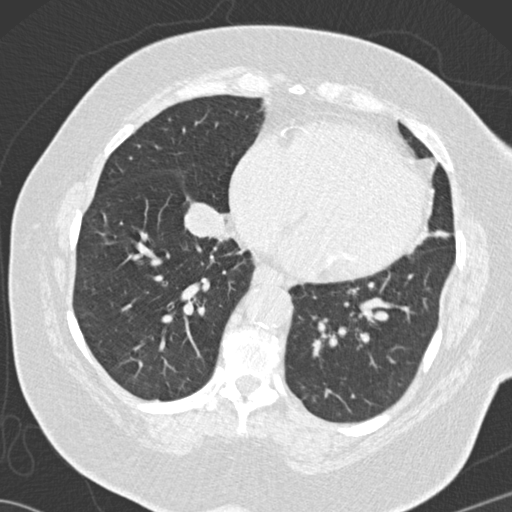
Low-dose screening chest CT, one axial slice. Position 50 of 146 along the scan axis. Reconstruction kernel B30f. 120 kVp. Lung window (W 1500 / L -600 HU). 512 × 512 image matrix.
Annotated regions visible in this slice (expert manual segmentation):
- lesion 3 (tumor, lower lobe of right lung): bounding box [x1, y1, x2, y2] px = [184, 203, 227, 237]